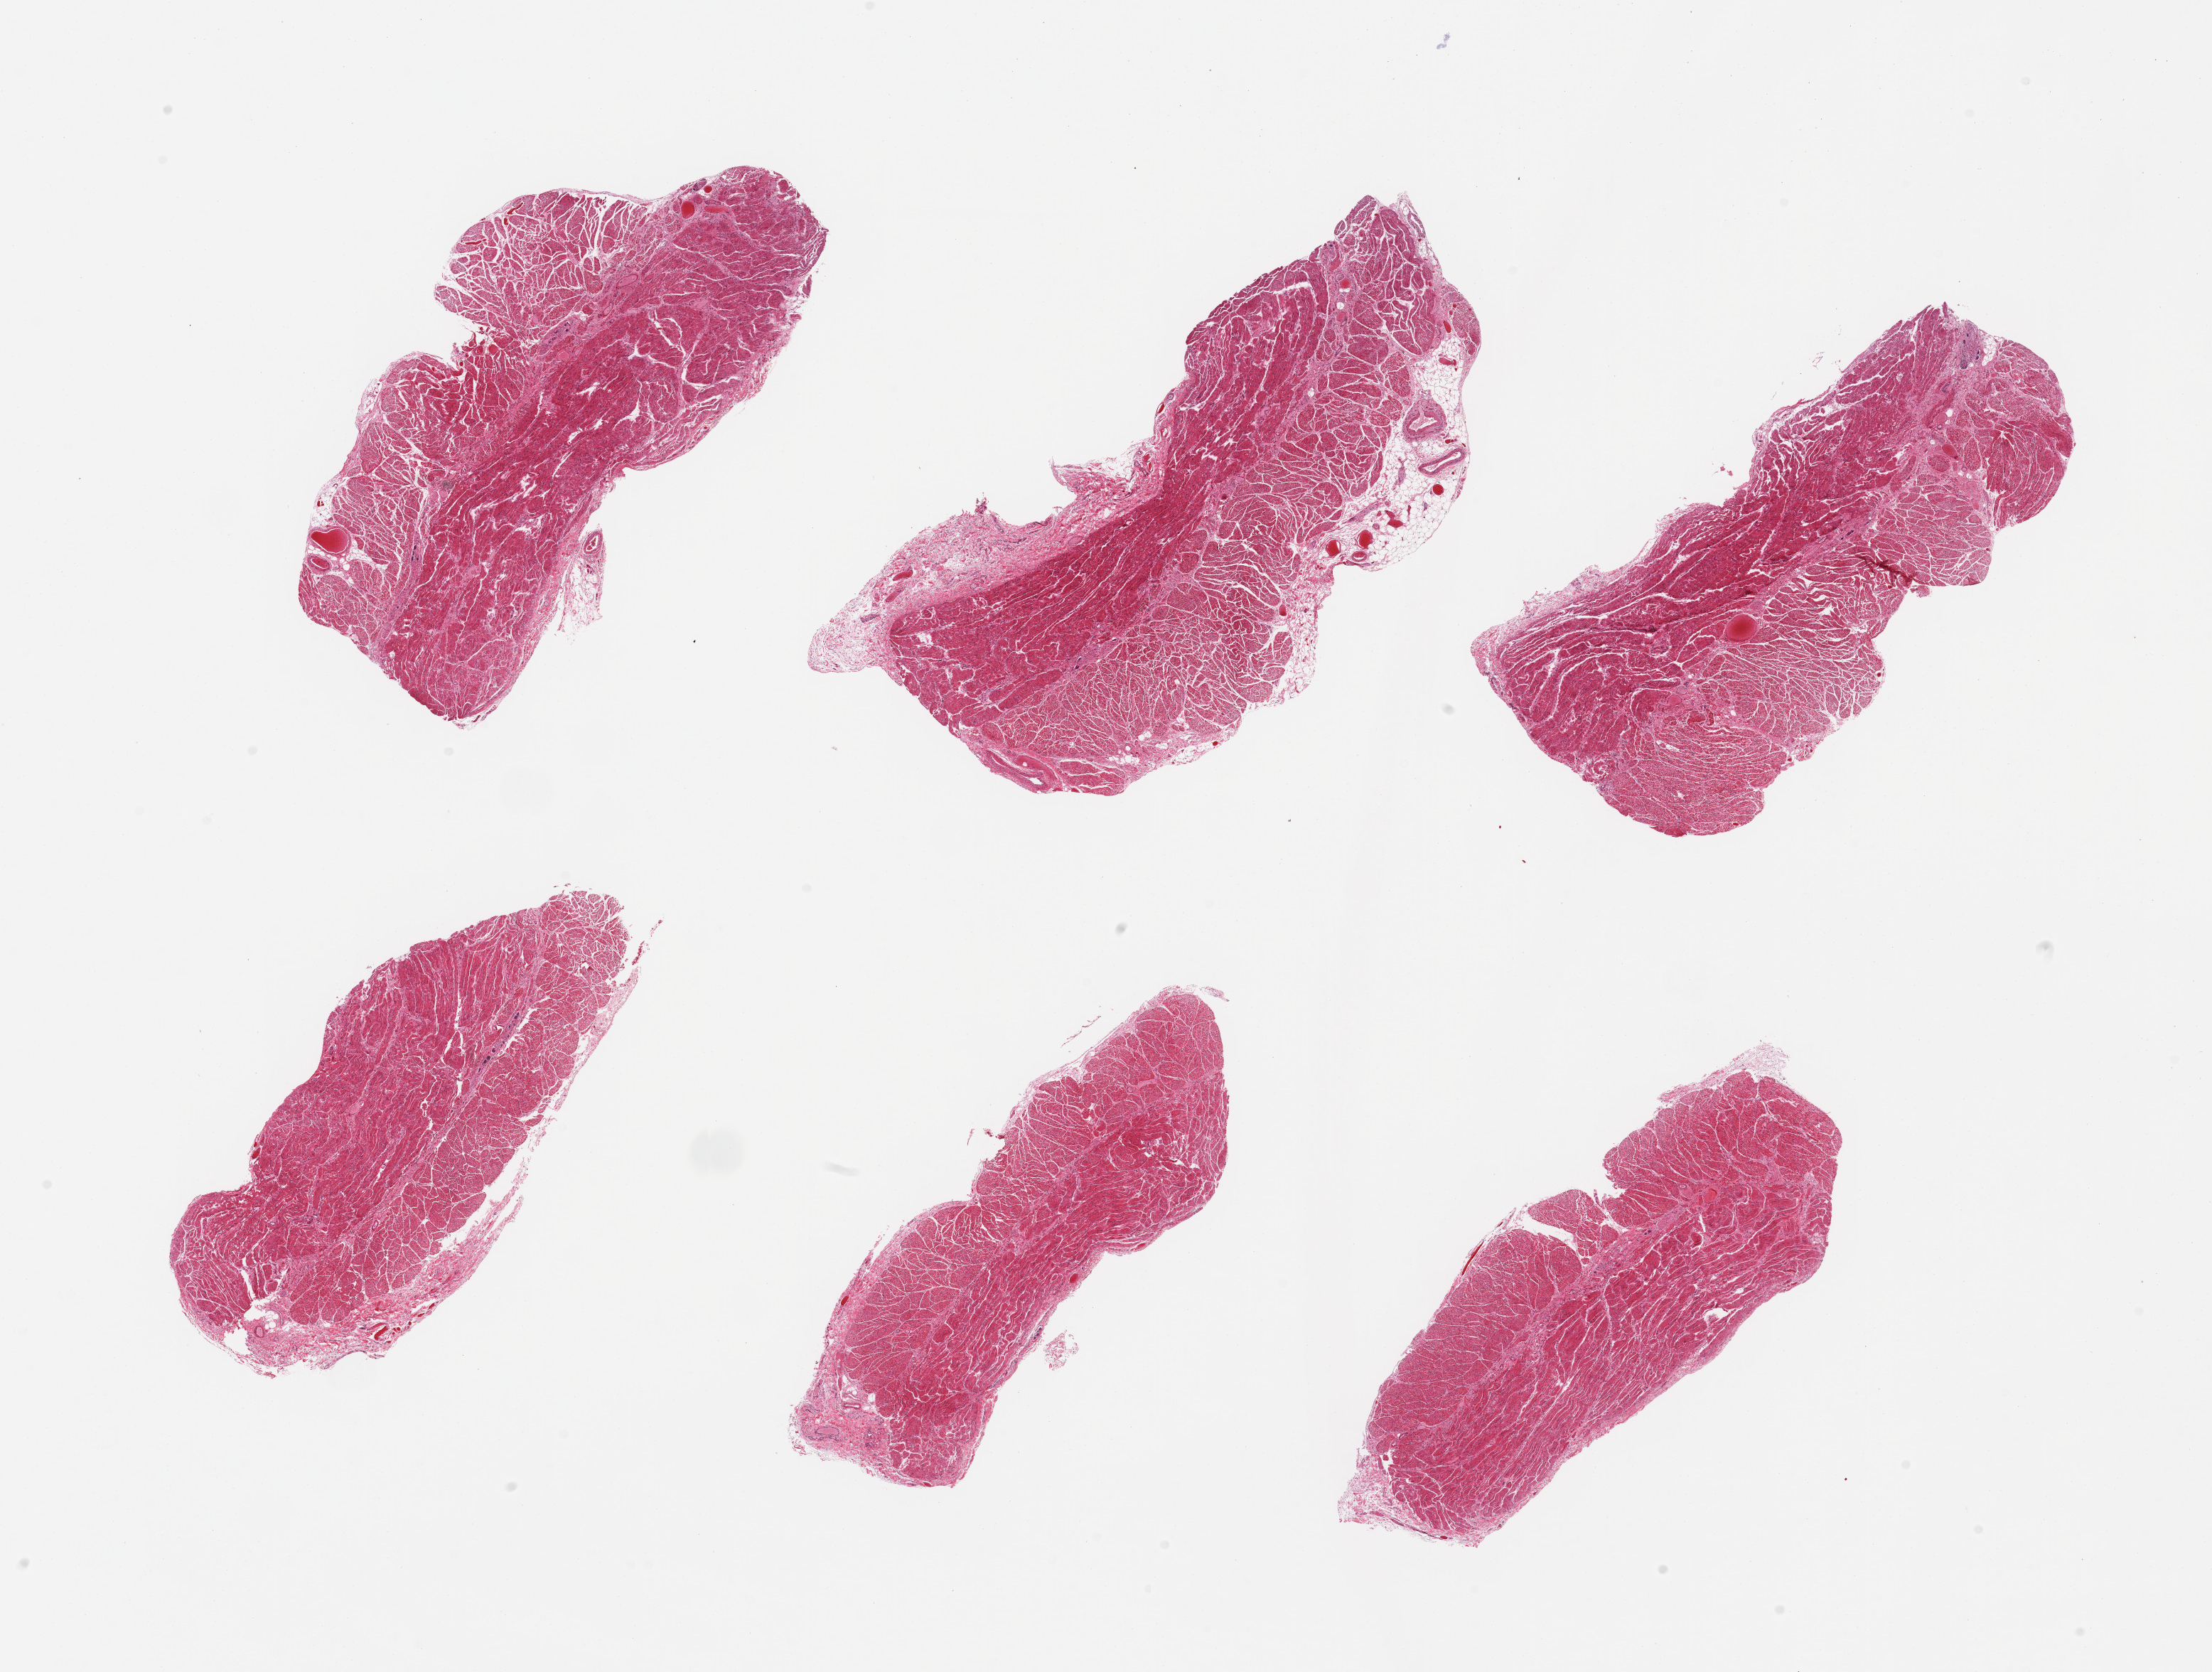
Whole-slide image, haematoxylin and eosin stain, low-resolution overview of the scanned area, about 24.6 x 18.6 mm (slide scanned at 20x), PAXgene-fixed paraffin-embedded (PFPE) section, section of gastroesophageal junction (target tissue), tissue donor sample. Male donor.
Review note (as recorded): 6 pieces; well preserved ganglion cells.